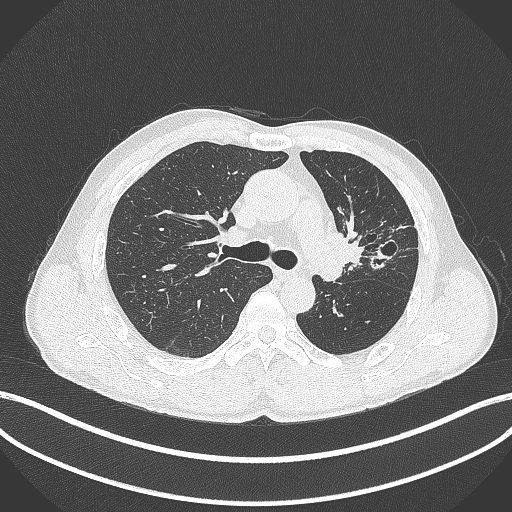
Chest CT, one axial slice. Position 270 of 429 along the scan axis. Reconstruction kernel B70f. Lung window (W 1500 / L -600 HU). 512 × 512 image matrix, field of view 400 × 400 mm. Patient: male, 57 years. Case-level facts recorded for this patient, not image findings: clinical TNM (as recorded): T2b N0 M0.
Structures marked on this image (rectangle marked by the reading radiologist):
- lung tumour (recorded histology: squamous cell carcinoma): bounding box <326,226,365,272> (left, top, right, bottom; pixels)